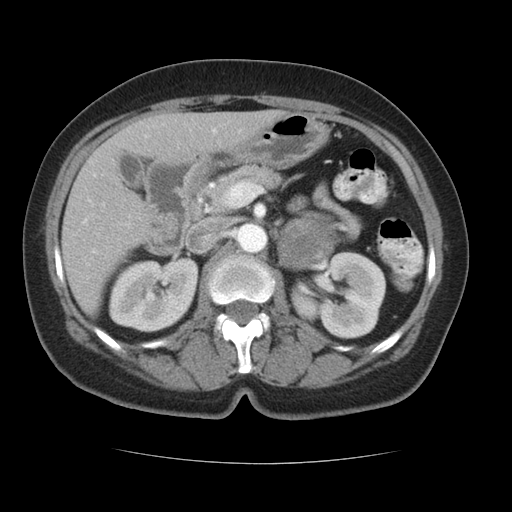
Contrast-enhanced abdominal CT, one axial slice. Position 62 of 96 along the scan axis. Reconstruction kernel STANDARD. 120 kVp. Intravenous contrast given. Soft-tissue window (W 400 / L 40 HU). 512 × 512 image matrix, field of view 348 × 348 mm. Female patient, age 66 years. Case-level facts recorded for this patient, not image findings: diagnosis: adrenocortical carcinoma; tumour side: left adrenal; tumour size at pathology: 5.5 cm; Ki-67 index: 15 %; stage (as recorded): 3.
Structures marked on this image (semi-automatically segmented with operator editing):
- mass: bounding box (x1, y1, x2, y2) in pixels: (279, 218, 340, 269)